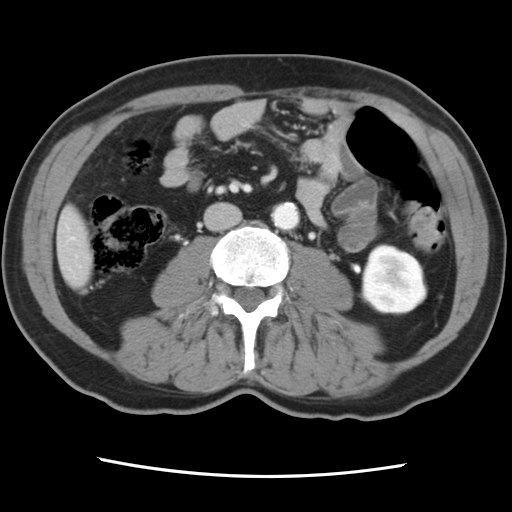
Contrast-enhanced abdominal CT, one axial slice; slice 16 of 83 in the series (ordered by position); 120 kVp; intravenous contrast given; soft-tissue window (W 400 / L 40 HU); 512 × 512 image matrix, field of view 321 × 321 mm. Male patient, age 69 years. From the clinical record (not read from this slice): diagnosis: colorectal cancer liver metastases, imaged before liver resection; multiple liver metastases: yes; largest metastasis: 3.5 cm; disease in both lobes: no.
Annotated regions visible in this slice (manually delineated by an expert):
- liver: bounding box (x1, y1, x2, y2) in pixels: (58, 210, 92, 286)
- planned liver remnant (the part of the liver to remain after resection): (59, 209, 92, 287)